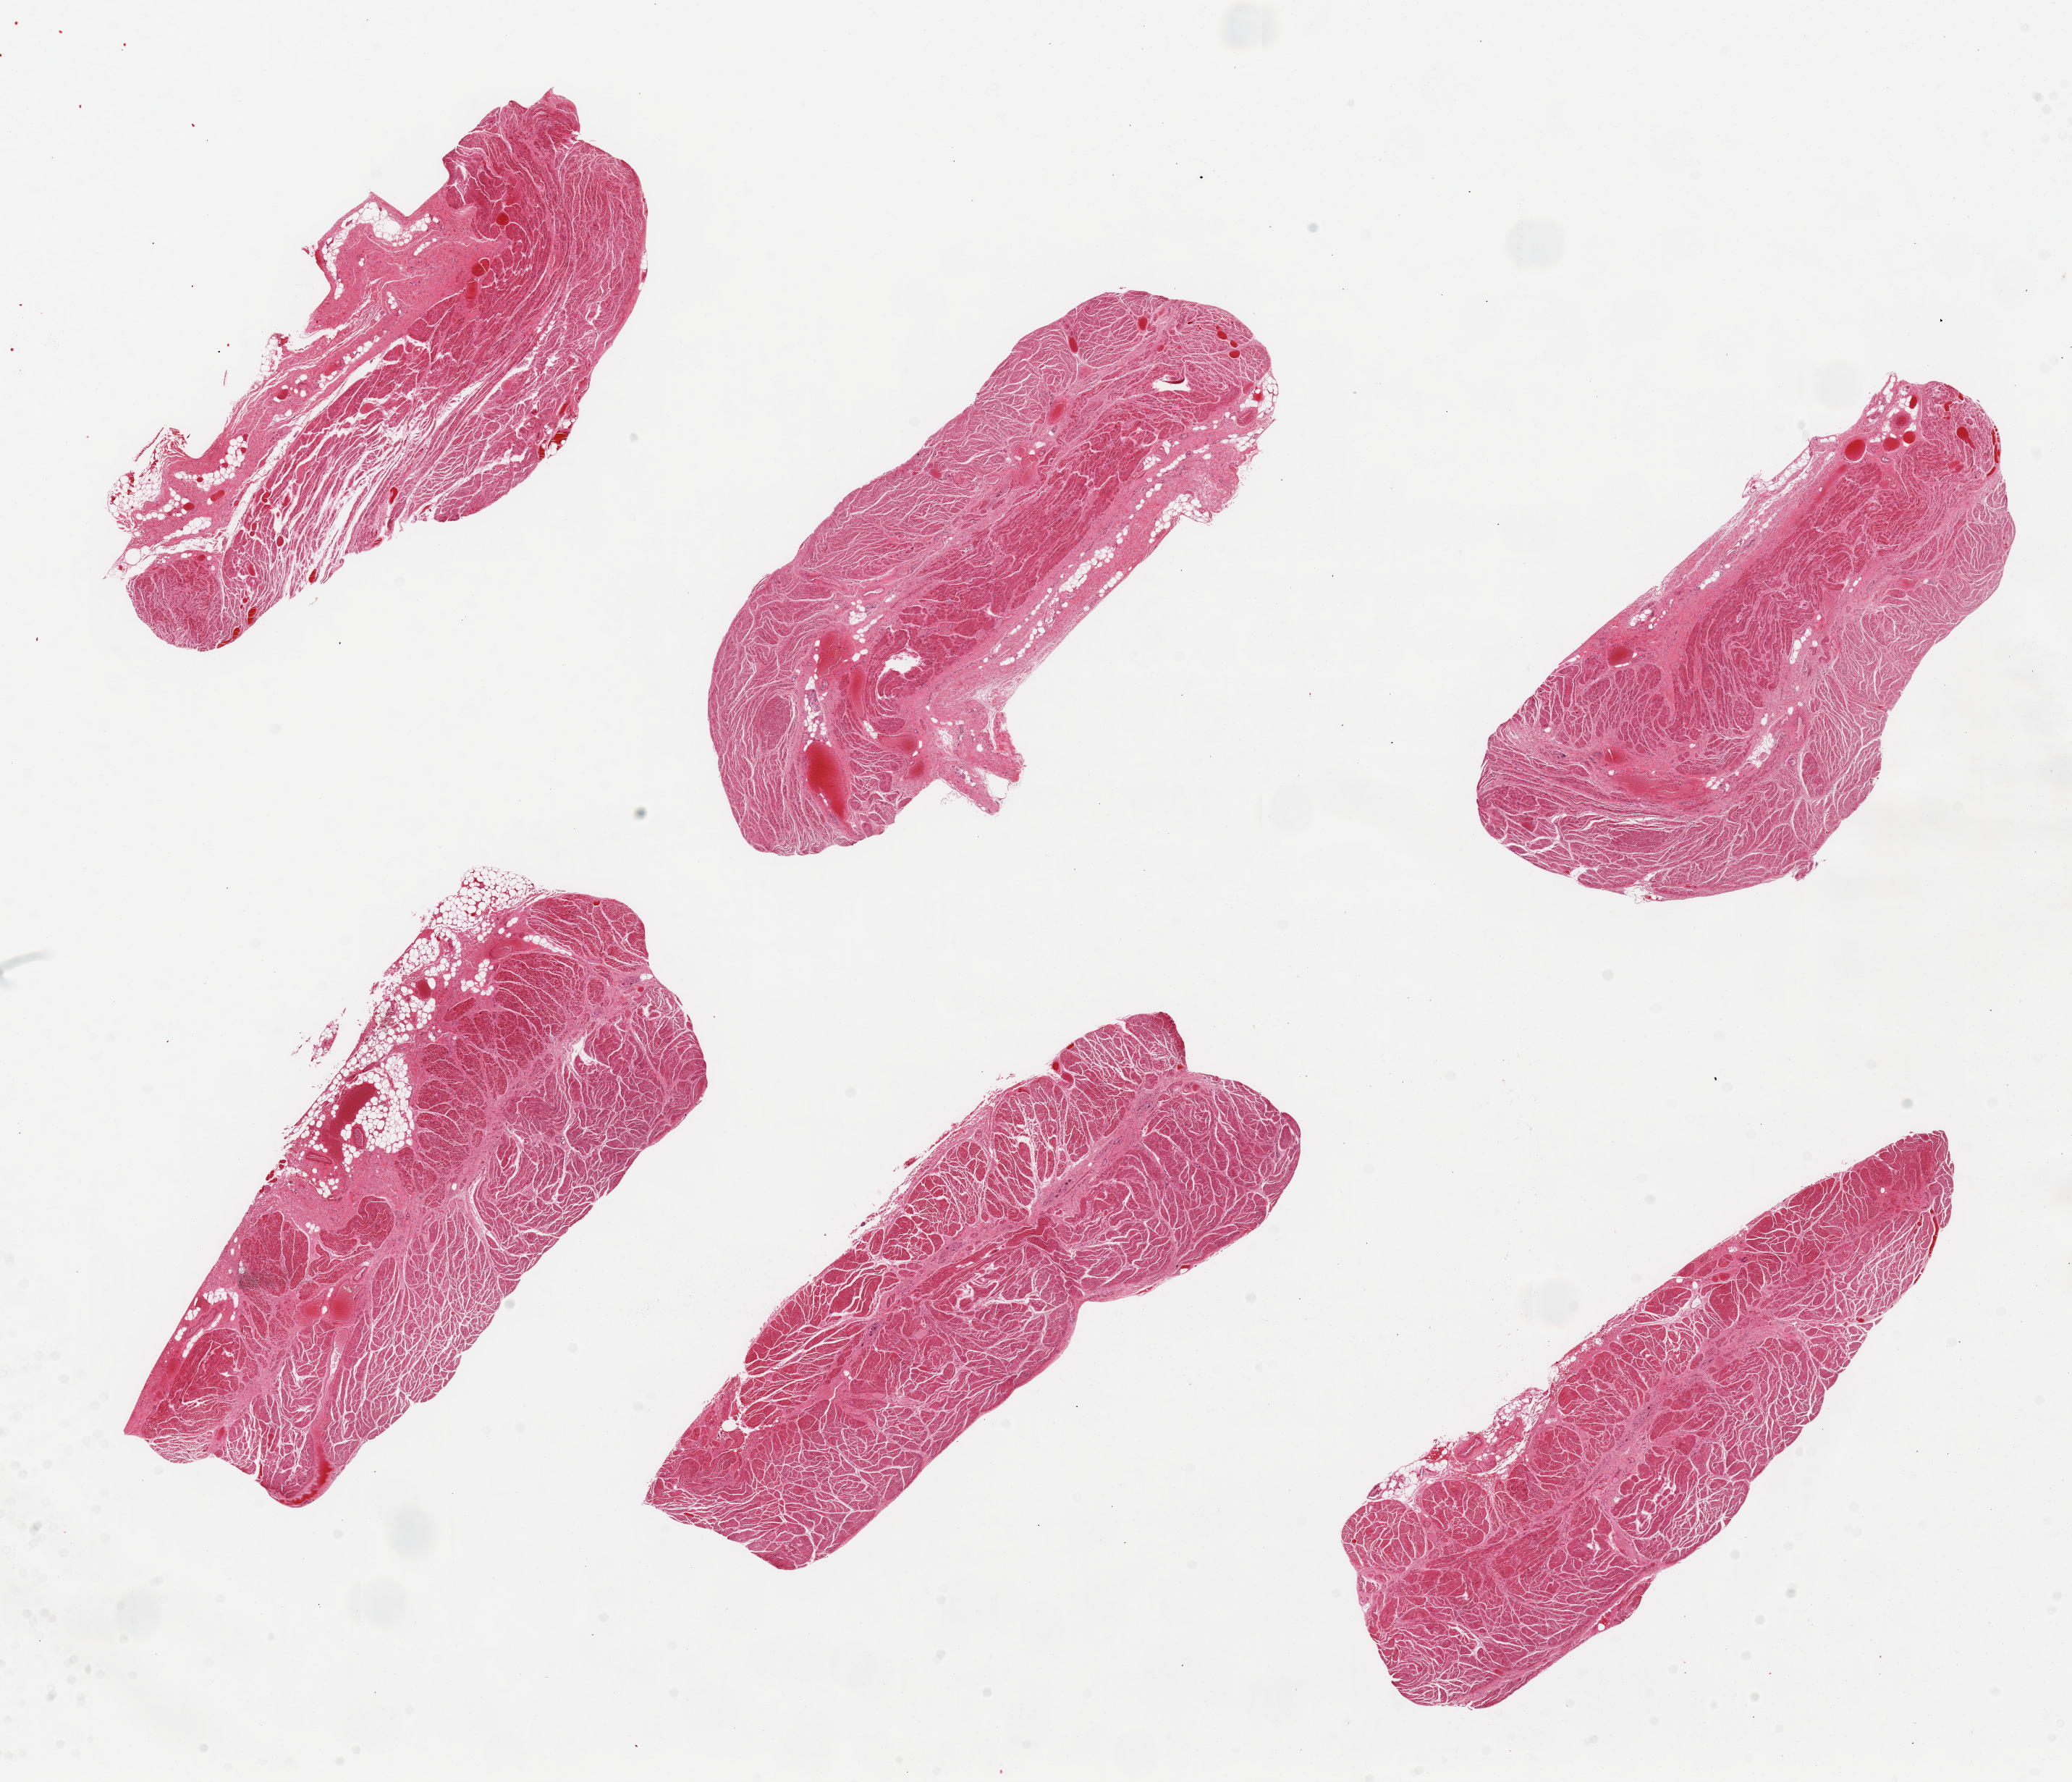
Digitized haematoxylin and eosin-stained section — shown as a low-resolution overview of the whole scanned area (about 22.6 x 19.5 mm, from a 20x scan), PAXgene-fixed paraffin-embedded (PFPE) section, sampled site (target tissue): gastroesophageal junction, tissue donor sample. Donor: male.
Pathologist's review note for this sample: 6 pieces, barely trace adherent fat, all muscularis; good specimens.